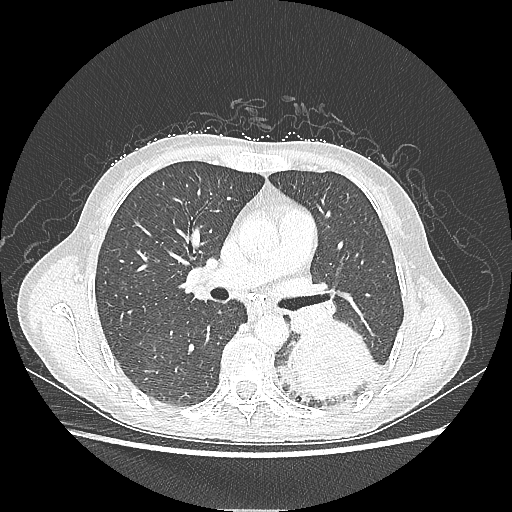
Chest CT, one axial slice. Position 126 of 220 along the scan axis. Reconstruction kernel LUNG. 80 kVp. Lung window (W 1500 / L -600 HU). 1.25 mm slice thickness. 512 × 512 image matrix, field of view 360 × 360 mm. Female patient, age 53 years. From the clinical record (not read from this slice): clinical TNM (as recorded): T3 N0 M0.
Annotated regions visible in this slice (rectangle marked by the reading radiologist):
- lung tumour (recorded histology: adenocarcinoma): bounding box [x1, y1, x2, y2] px = [278, 319, 375, 401]